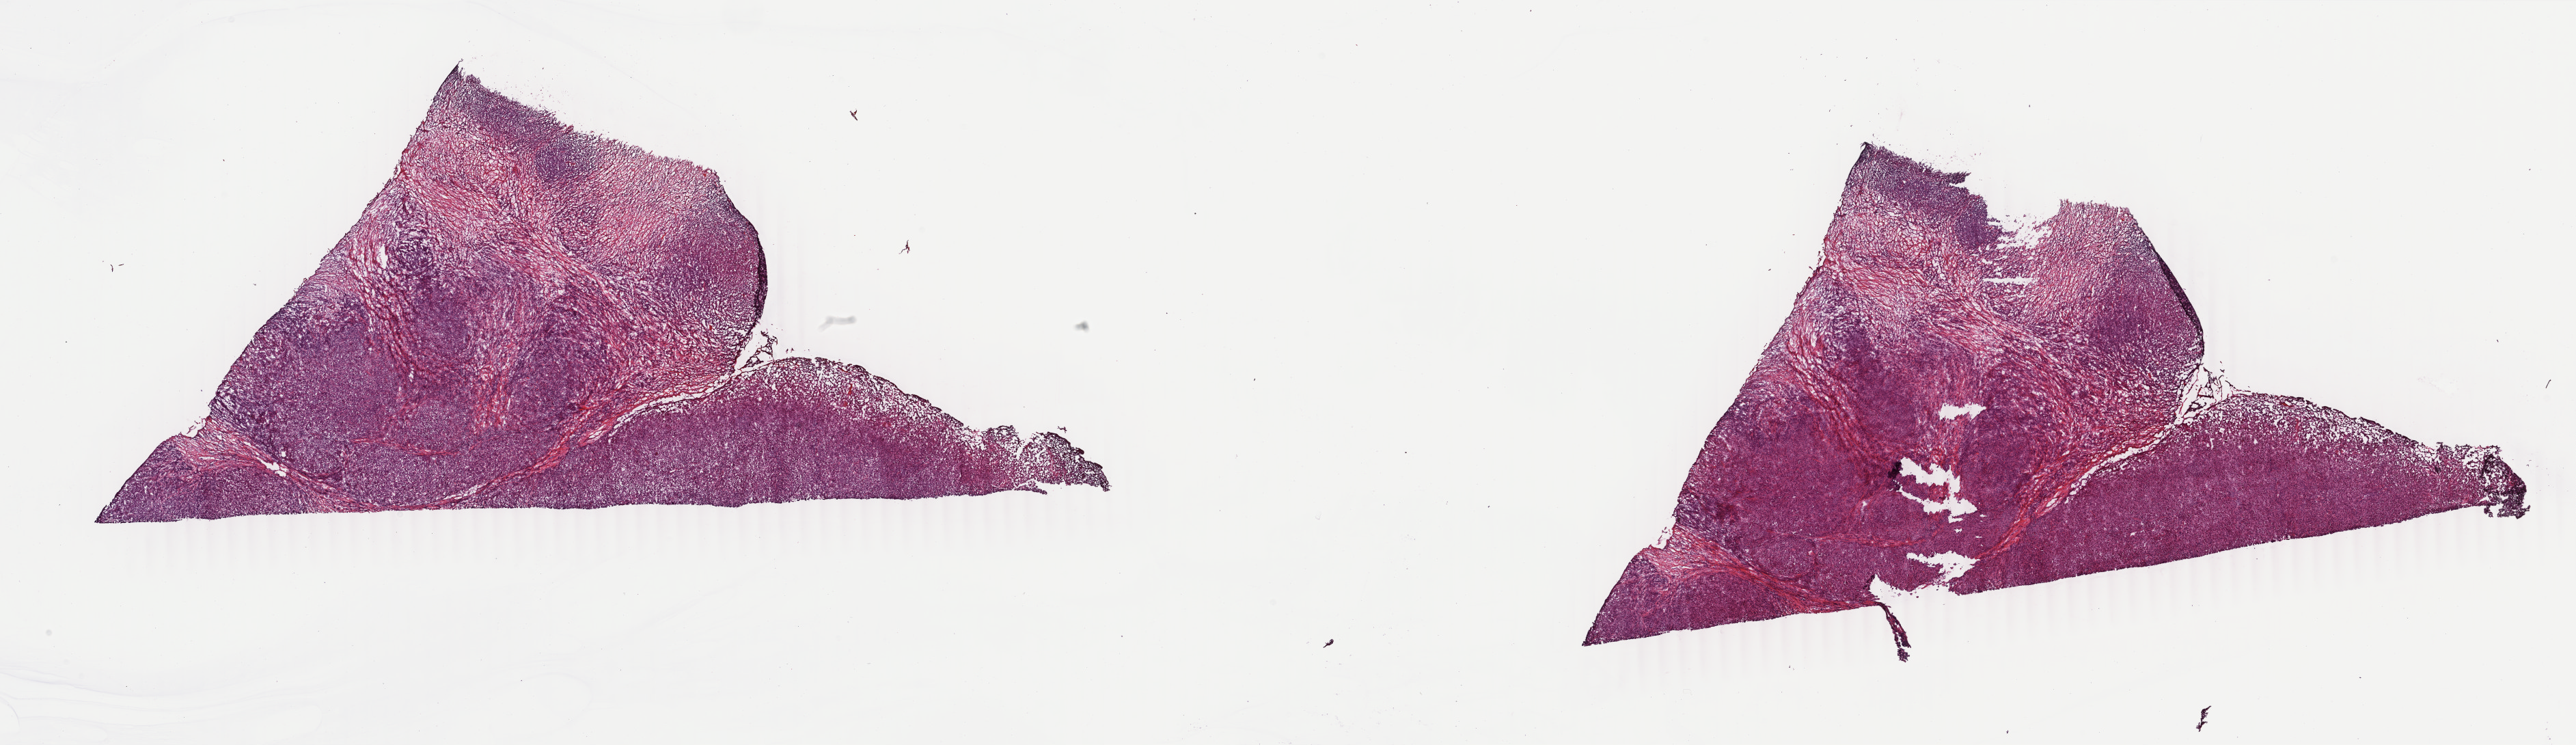
Digitized H&E-stained tissue section (whole slide) — a low-resolution overview of the entire scanned area, about 30.0 x 8.7 mm. Frozen section from the top of the tissue portion. Metastatic tumour sample, sampled site: lymph nodes of axilla or arm. Patient: female, age at initial diagnosis 57 years. Composition of this section per pathologist review: tumour cells 100%, tumour nuclei 88%.
This section: metastatic tumour tissue. Patient diagnosis: Malignant melanoma, NOS.